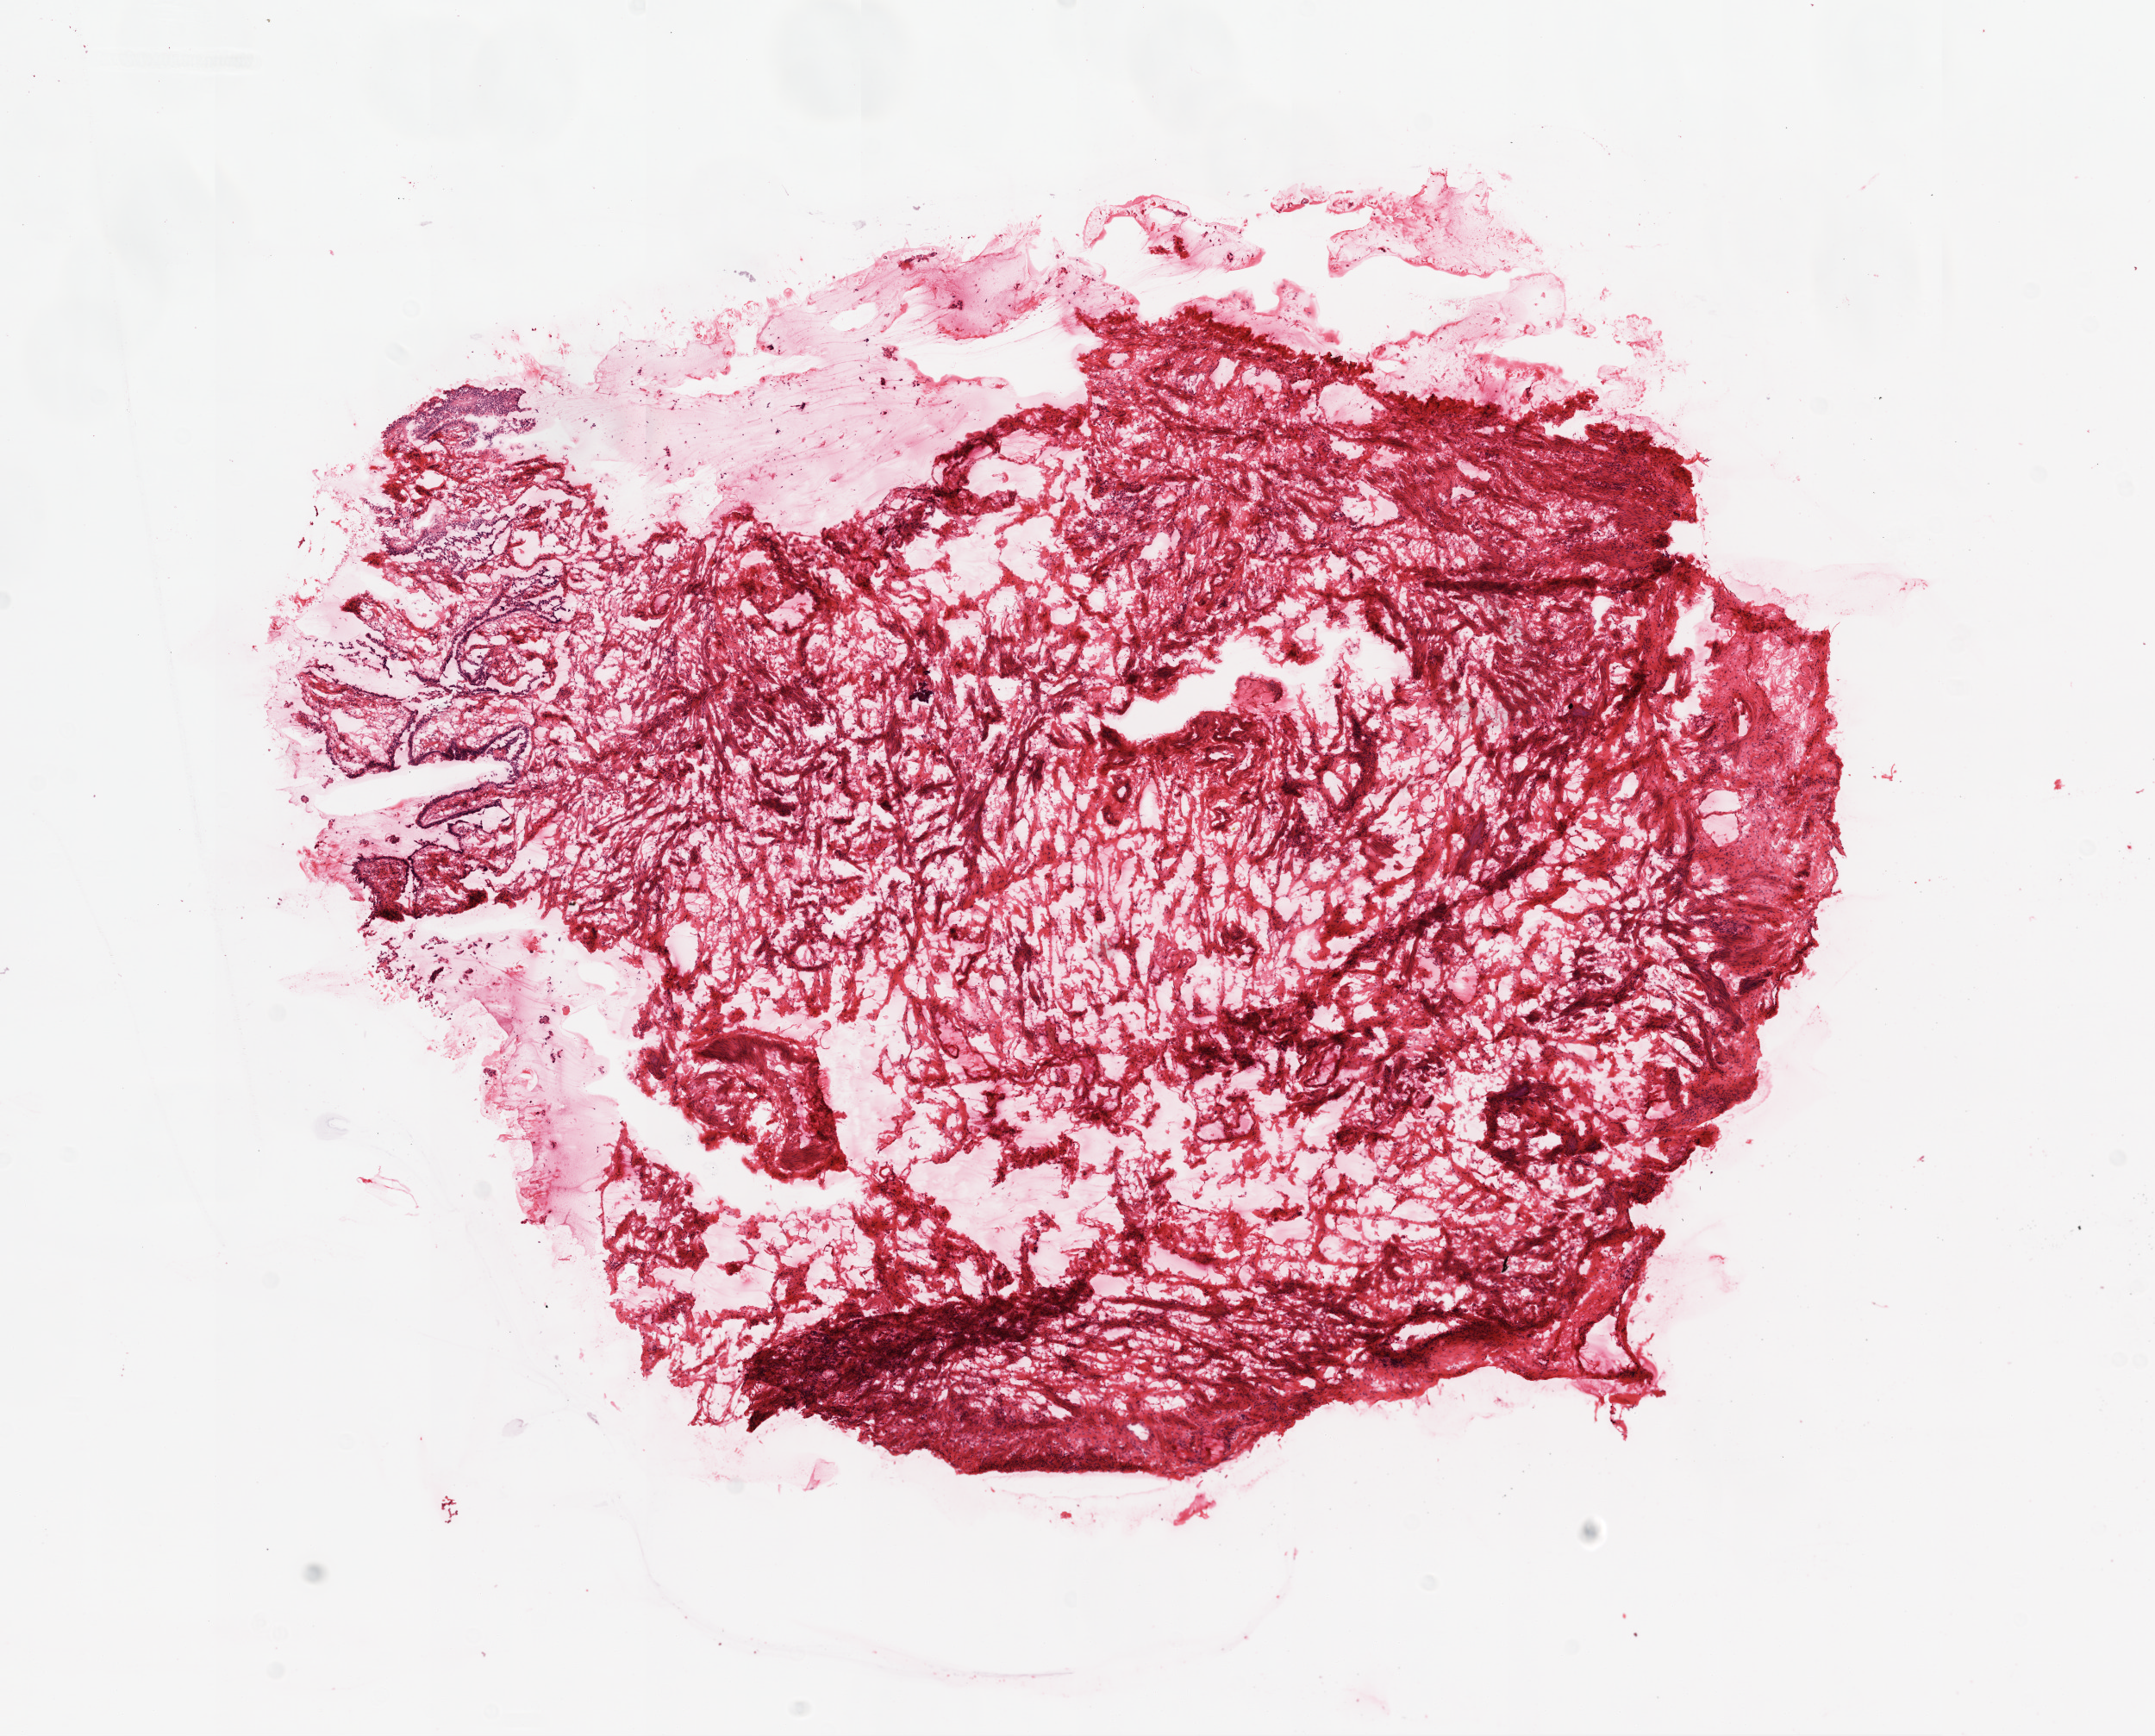
Digitized Hematoxylin and eosin (H&E) stained tissue section (whole slide), whole scanned area (about 10.0 x 8.1 mm, slide scanned at 20x) shown as a low-resolution overview, frozen section from the top of the tissue portion, ovary, solid tissue normal (non-tumour tissue) sample. Female patient; age at initial diagnosis 55 years.
• this section: solid tissue normal sample (biorepository sample class)
• patient diagnosis: Serous cystadenocarcinoma, NOS